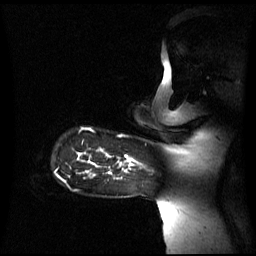
Breast MRI (dynamic contrast-enhanced), one sagittal slice. Slice 52 of 60 in the series (ordered by position). Dynamic contrast-enhanced series, image 2 of 3 at this slice position (ordered by acquisition). 1.5 T. TE 4.2 ms, TR 8.4 ms. 2.6 mm slice thickness. 256 × 256 image matrix, field of view 270 × 270 mm. Patient: female, 39 years. Case-level facts recorded for this patient, not image findings: setting: breast cancer imaged before/during neoadjuvant chemotherapy; receptor status: triple-negative.
Structures marked on this image (semi-automatically segmented with operator editing):
- analysis volume of interest (the breast-tissue region the enhancement analysis was run in; not a lesion): bounding box <108,159,138,174> (left, top, right, bottom; pixels)
- tumour enhancement mask (voxels above the 70 % enhancement threshold inside the analysis volume of interest): <109,159,134,174>